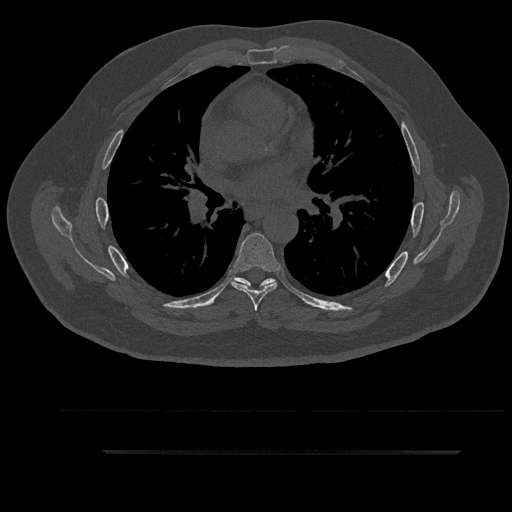
CT including the spine, one axial slice. Slice 566 of 797 in the series (ordered by position). 120 kVp. Bone window (W 1800 / L 400 HU). 512 × 512 image matrix, field of view 432 × 432 mm. Patient: male, 63 years. From the clinical record (not read from this slice): primary cancer: renal; vertebrae with lytic lesions (as recorded): T8.
Structures marked on this image (semi-automatic segmentation, software-assisted and operator-edited):
- T5 vertebra: bounding box [x1, y1, x2, y2] px = [235, 278, 266, 290]
- T6 vertebra: [231, 233, 280, 311]
- T7 vertebra: [235, 278, 276, 285]